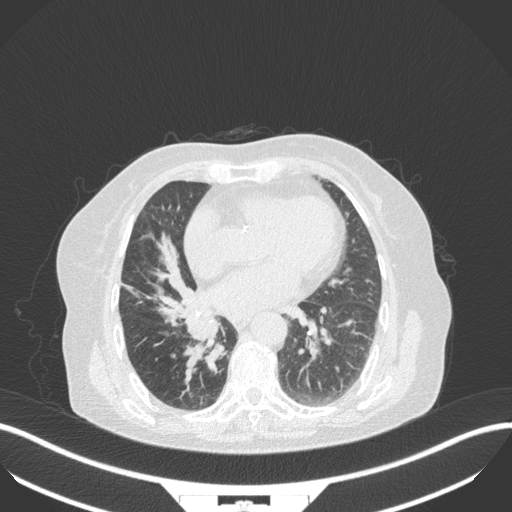
Chest CT, one axial slice; position 132 of 329 along the scan axis; lung window (W 1500 / L -600 HU); 512 × 512 image matrix, field of view 400 × 400 mm. Female patient, age 75 years. Case-level facts recorded for this patient, not image findings: clinical TNM (as recorded): T1b N0 M1a; histopathological grade: G1.
Annotated regions visible in this slice (rectangle marked by the reading radiologist):
- lung tumour (recorded histology: squamous cell carcinoma): bounding box [x1, y1, x2, y2] px = [178, 311, 222, 378]